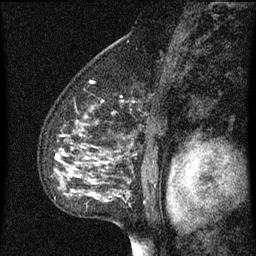
Breast MRI (dynamic contrast-enhanced), one sagittal slice. Slice 48 of 60 in the series (ordered by position). Dynamic contrast-enhanced series, image 2 of 3 at this slice position (ordered by acquisition). 1.5 T. TE 4.2 ms, TR 8 ms. 2 mm slice thickness. 256 × 256 image matrix. Patient: female, 55 years.
Annotated regions visible in this slice (semi-automatic segmentation, software-assisted and operator-edited):
- analysis volume of interest (the breast-tissue region the enhancement analysis was run in; not a lesion): bounding box (x1, y1, x2, y2) in pixels: (42, 82, 157, 151)
- tumour enhancement mask (voxels above the 70 % enhancement threshold inside the analysis volume of interest): (80, 102, 103, 135)